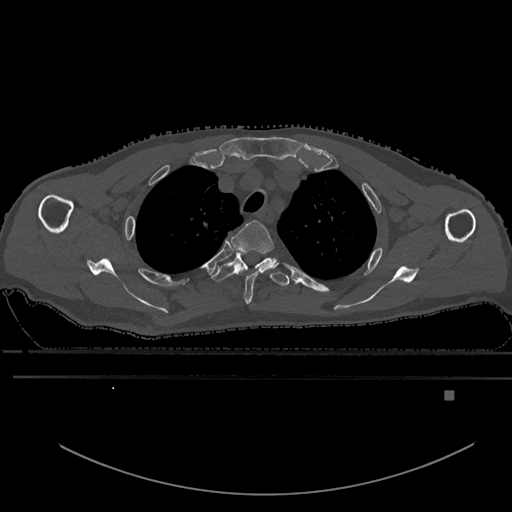
CT including the spine, one axial slice. Position 473 of 969 along the scan axis. Bone window (W 1800 / L 400 HU). 0.5 mm slice thickness. 512 × 512 image matrix, field of view 456 × 456 mm. Patient: male, 82 years. Case-level facts recorded for this patient, not image findings: primary cancer: prostate; vertebrae with lytic lesions (as recorded): T11, T9, T8, T2.
Outlined on this slice (semi-automatically segmented with operator editing):
- T2 vertebra: box from (x=231, y=220) to (x=277, y=304) px
- T3 vertebra: (x=211, y=251)–(x=289, y=287)